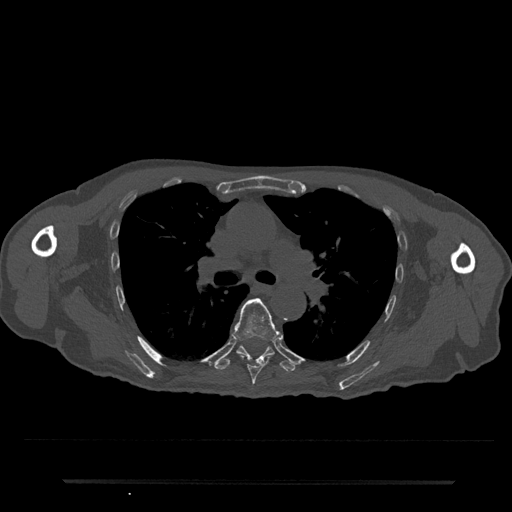
CT including the spine, one axial slice; slice 511 of 797 in the series (ordered by position); 120 kVp; bone window (W 1800 / L 400 HU); 0.5 mm slice thickness; 512 × 512 image matrix, field of view 427 × 427 mm. Male patient, age 74 years. From the clinical record (not read from this slice): primary cancer: prostate.
Outlined on this slice (semi-automatically segmented with operator editing):
- T6 vertebra: bounding box [x1, y1, x2, y2] px = [233, 298, 280, 385]
- T7 vertebra: [215, 346, 295, 371]